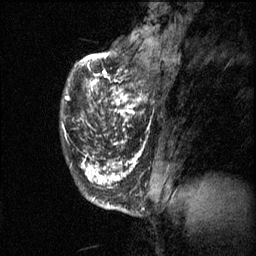
Breast MRI (dynamic contrast-enhanced), one sagittal slice. Slice 14 of 60 in the series (ordered by position). 3 images stored at this slice position (order not interpretable as contrast timing). 1.5 T. TE 4.2 ms, TR 11.1 ms. 2 mm slice thickness. 256 × 256 image matrix. Female patient, age 50 years.
Structures marked on this image (semi-automatic segmentation, software-assisted and operator-edited):
- analysis volume of interest (the breast-tissue region the enhancement analysis was run in; not a lesion): bounding box [x1, y1, x2, y2] px = [77, 68, 153, 141]
- tumour enhancement mask (voxels above the 70 % enhancement threshold inside the analysis volume of interest): [78, 68, 142, 141]